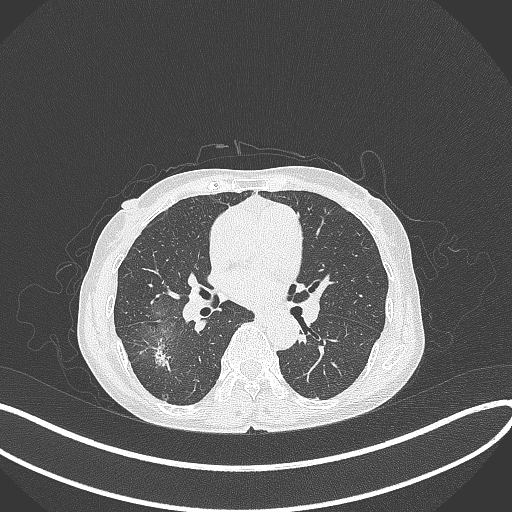
Chest CT, one axial slice; slice 205 of 371 in the series (ordered by position); reconstruction kernel B70f; 120 kVp; lung window (W 1500 / L -600 HU); 1 mm slice thickness; 512 × 512 image matrix, field of view 400 × 400 mm. Patient: female, 69 years. From the clinical record (not read from this slice): clinical TNM (as recorded): T1b N0 M0.
Outlined on this slice (bounding box drawn by a radiologist):
- lung tumour (recorded histology: adenocarcinoma): box from (x=148, y=333) to (x=178, y=375) px